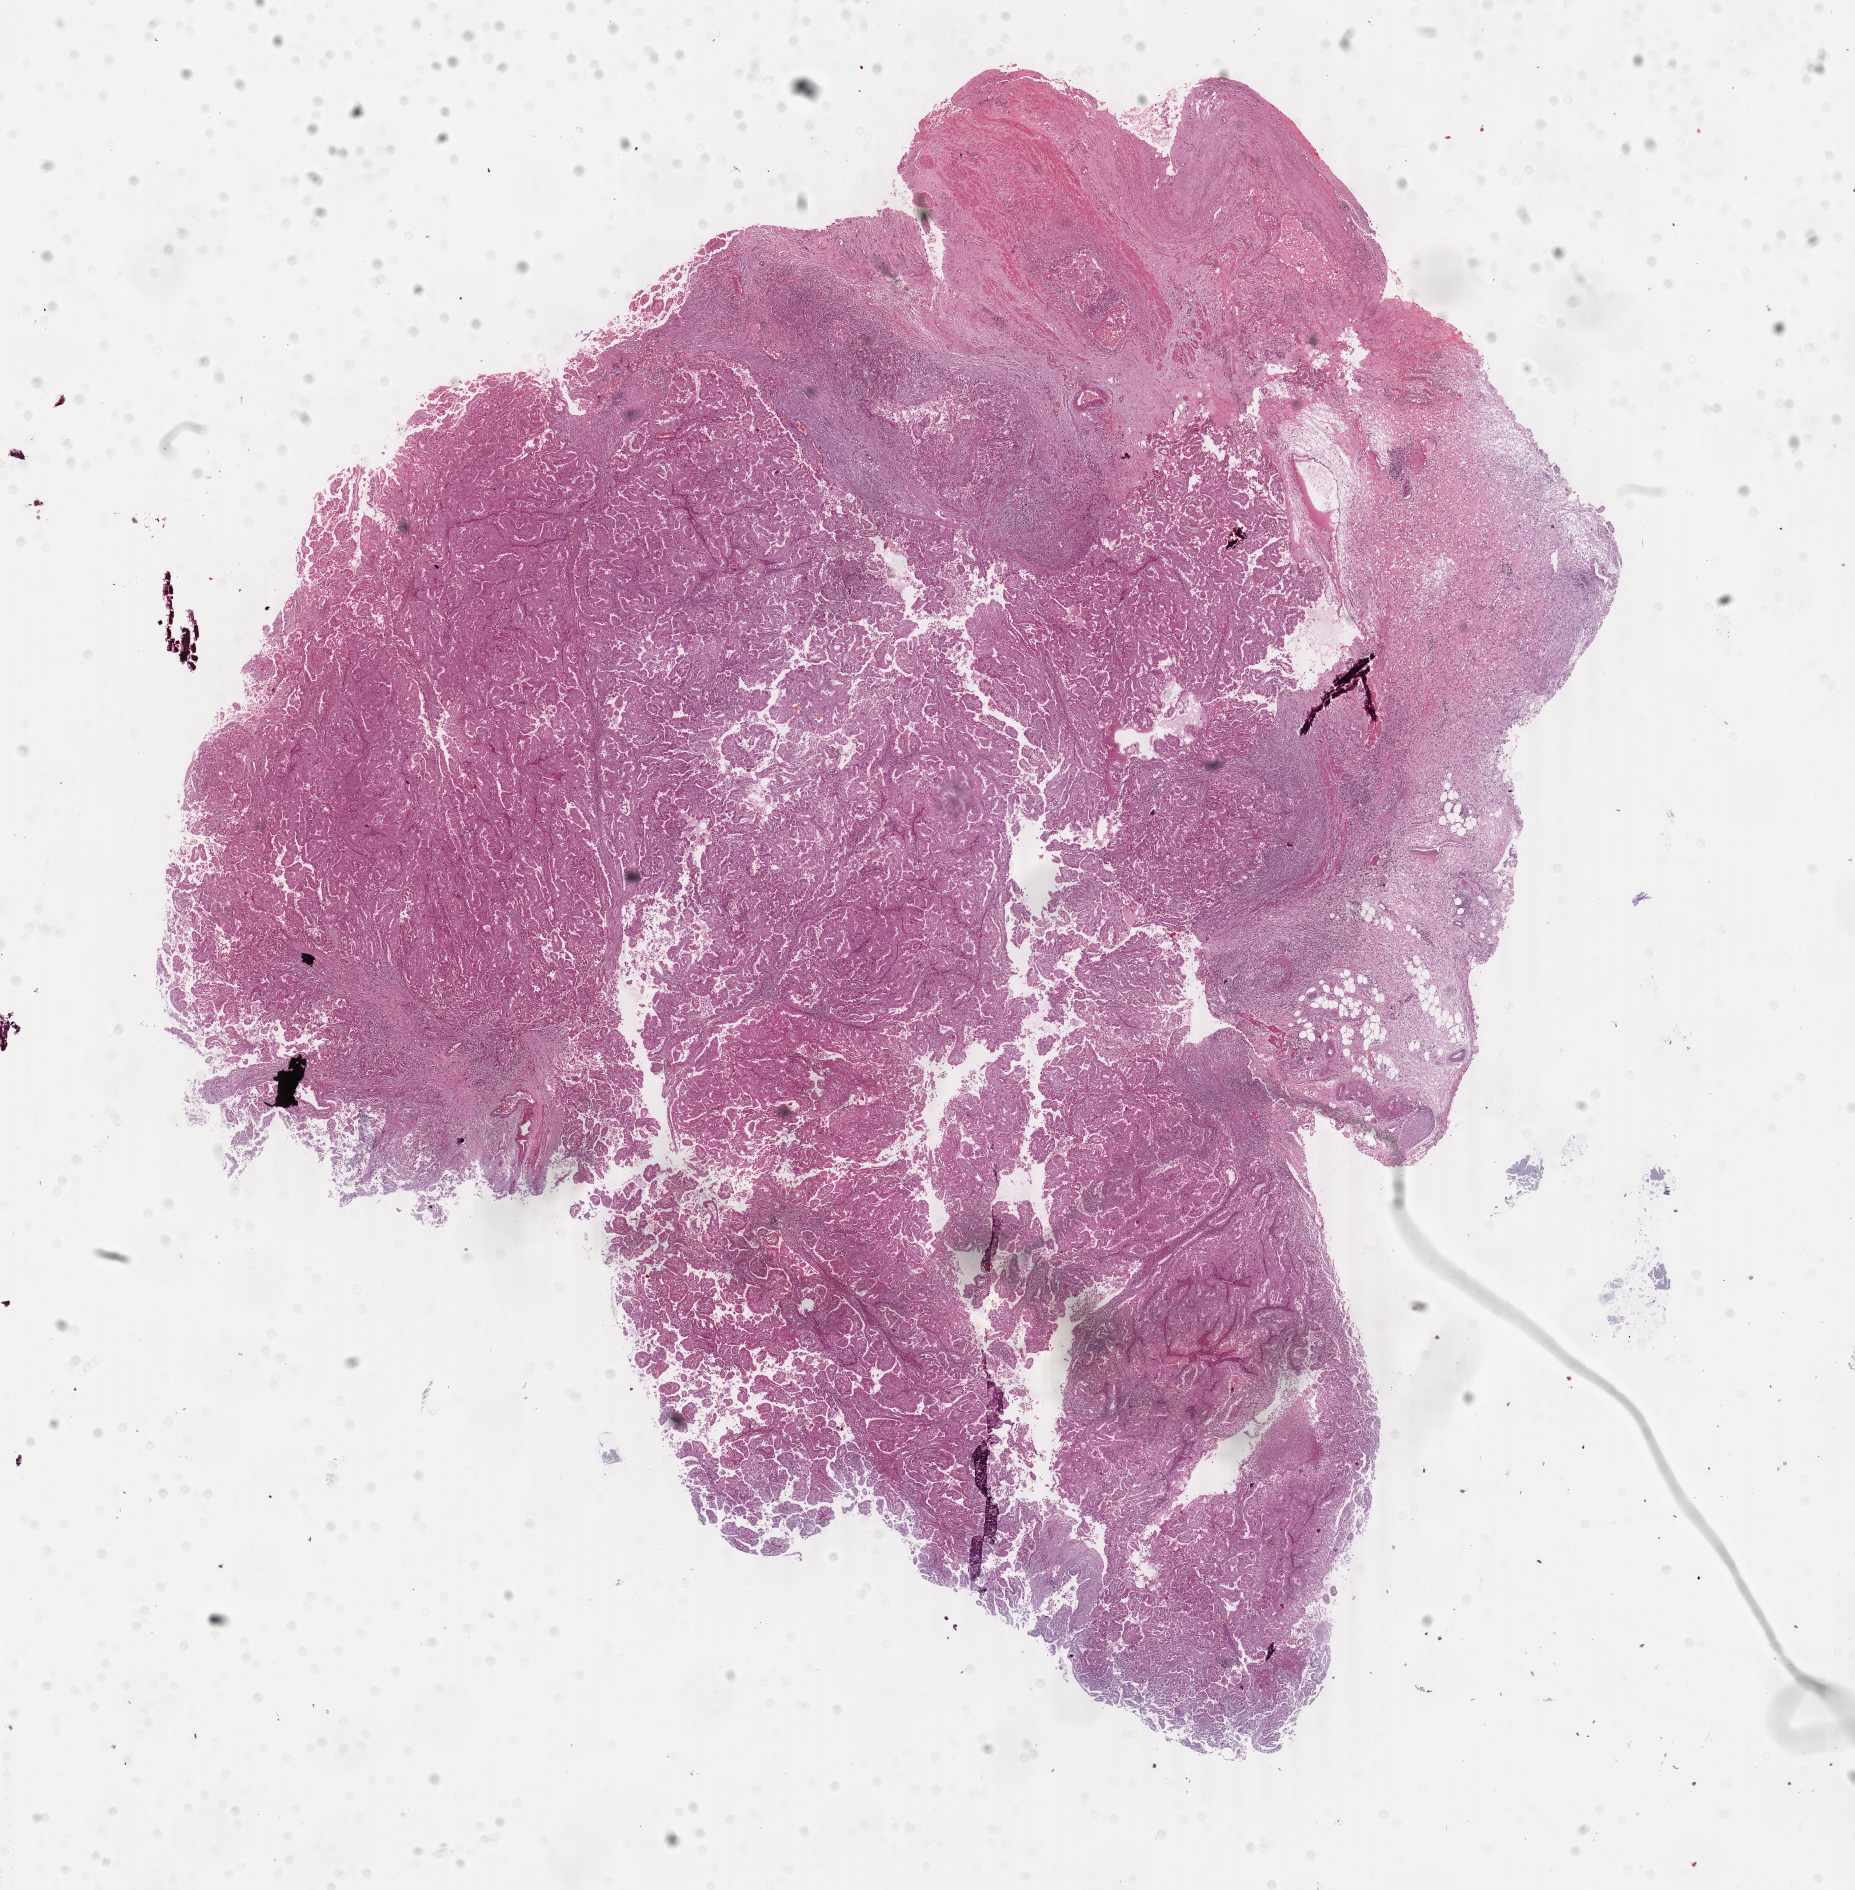
Hematoxylin and eosin (H&E) stained whole-slide image — whole scanned area (about 14.8 x 15.0 mm, from a 40x scan) shown as a low-resolution overview. FFPE section. Sample: primary tumour, kidney. Female, age 37 years at initial diagnosis.
Pathologic diagnosis: Papillary adenocarcinoma, NOS. AJCC pathologic stage: III. Laterality: left.